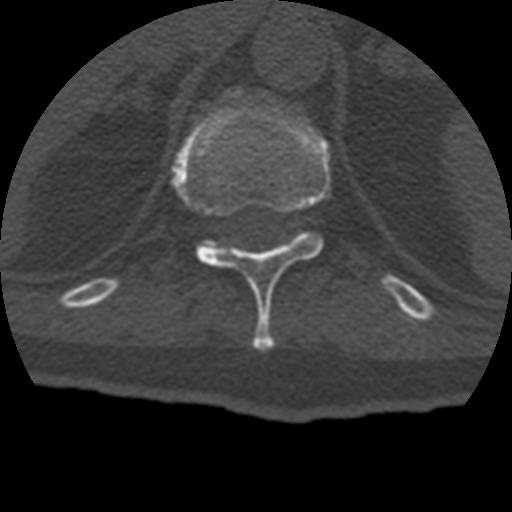
CT including the spine, one axial slice; position 191 of 399 along the scan axis; reconstruction kernel STANDARD; 120 kVp; bone window (W 1800 / L 400 HU); 512 × 512 image matrix, field of view 160 × 160 mm. Patient age 69 years. From the clinical record (not read from this slice): primary cancer: prostate.
Outlined on this slice (semi-automatically segmented with operator editing):
- T11 vertebra: bounding box <171,102,331,350> (left, top, right, bottom; pixels)